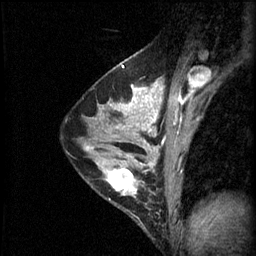
Breast MRI (dynamic contrast-enhanced), one sagittal slice; position 36 of 60 along the scan axis; 3 images stored at this slice position (order not interpretable as contrast timing); 1.5 T; TE 4.2 ms, TR 11 ms; 256 × 256 image matrix, field of view 180 × 180 mm. Female patient, age 29 years.
Structures marked on this image (semi-automatic segmentation, software-assisted and operator-edited):
- analysis volume of interest (the breast-tissue region the enhancement analysis was run in; not a lesion): box from (x=96, y=164) to (x=153, y=225) px
- tumour enhancement mask (voxels above the 70 % enhancement threshold inside the analysis volume of interest): (x=105, y=166)–(x=153, y=195)